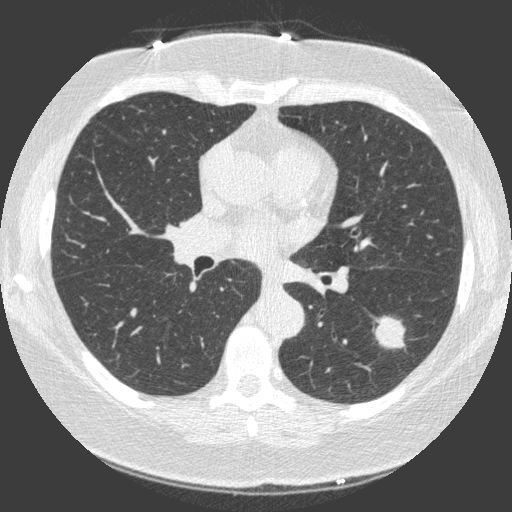
Low-dose screening chest CT, one axial slice. Position 87 of 149 along the scan axis. 120 kVp. Lung window (W 1500 / L -600 HU). 1 mm slice thickness. 512 × 512 image matrix, field of view 330 × 330 mm.
Structures marked on this image (outlined manually by an expert reader):
- lesion 1 (tumor, lower lobe of left lung): bounding box [x1, y1, x2, y2] px = [375, 316, 405, 348]